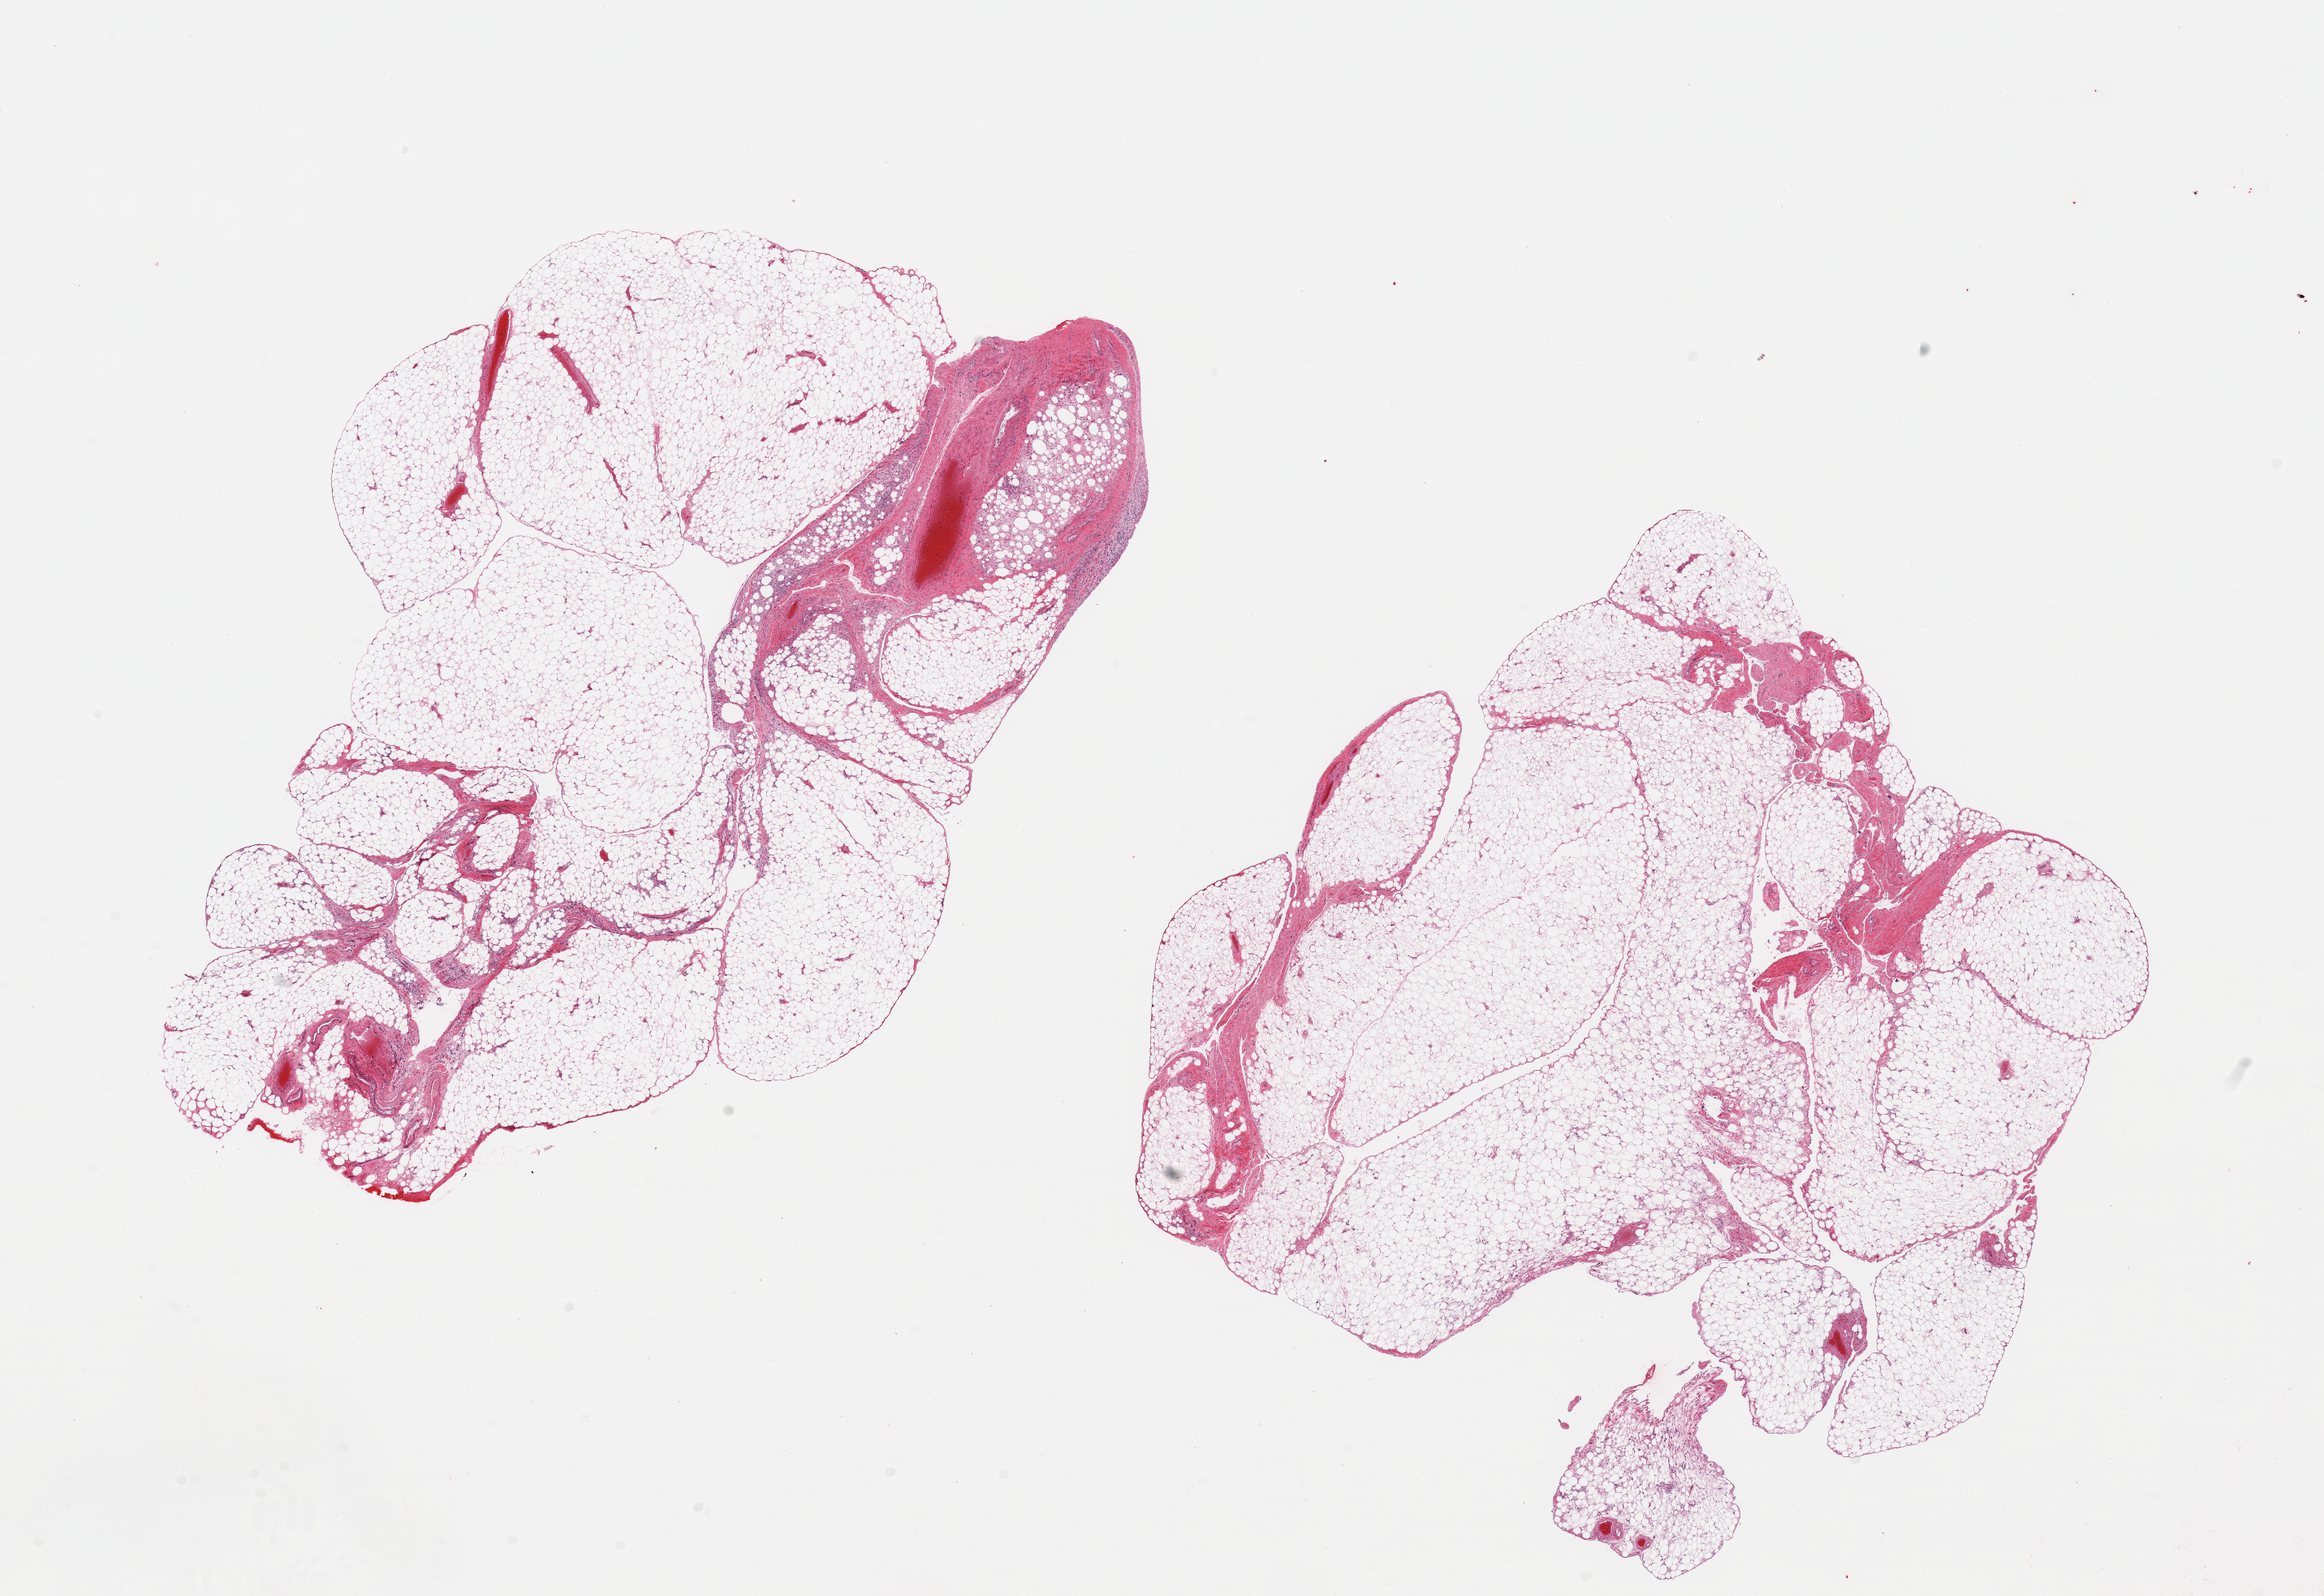
Whole-slide image, haematoxylin and eosin stain, shown as a low-resolution overview of the whole scanned area (about 22.6 x 15.5 mm, slide scanned at 20x), PAXgene-fixed paraffin-embedded (PFPE) section, section of omentum (target tissue), tissue donor sample. Male donor.
Review note (as recorded): 2 pieces; 5% stromal content.